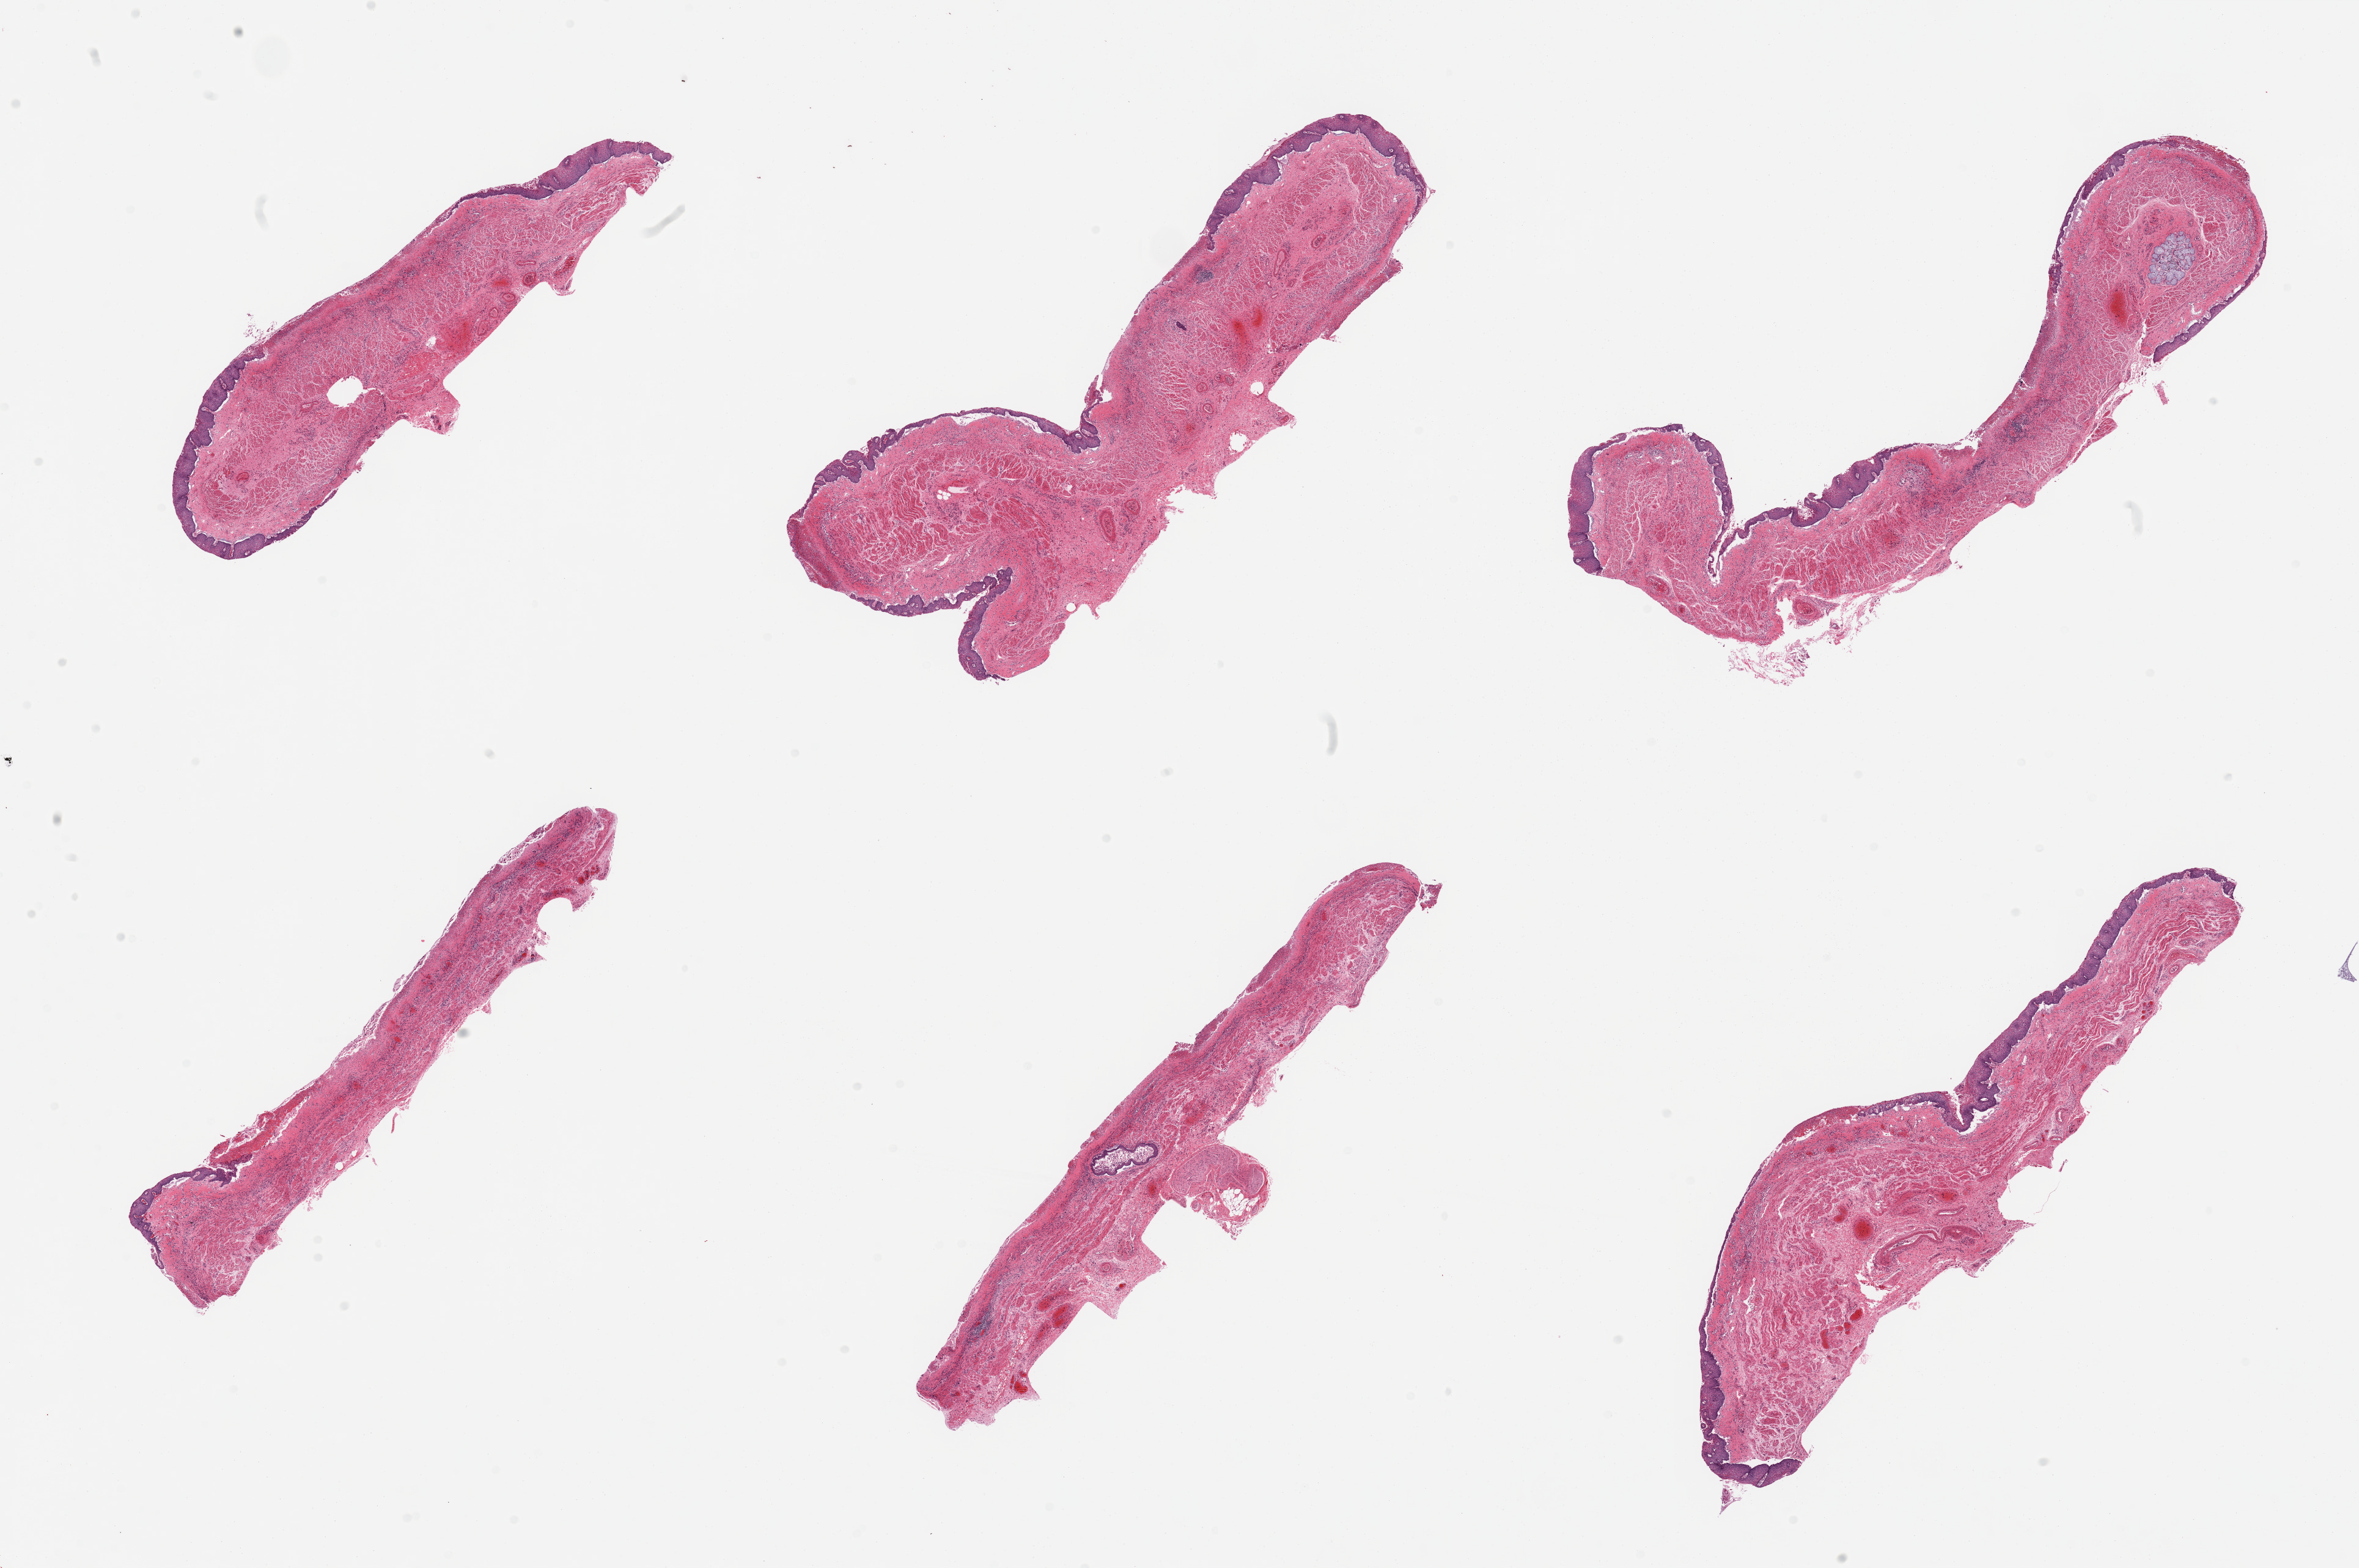
Whole-slide image, H&E stain, a low-resolution overview of the entire scanned area, about 30.5 x 20.3 mm (slide scanned at 20x); PAXgene-fixed paraffin-embedded (PFPE) section; section of esophageal mucous membrane (target tissue); donor tissue sample. Donor sex: male.
Review note (as recorded): 6 pieces, squamous mucosa ~5-10% thickness, partially sloughing.